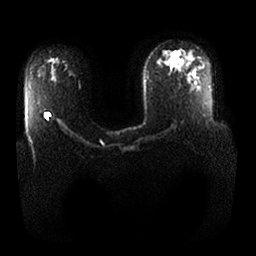
Breast MRI, one axial slice. Slice 13 of 25 in the series (ordered by position). Diffusion-weighted series; image 2 of 4 stored at this slice position (different b-values; order by instance number). 1.5 T. 256 × 256 image matrix, field of view 380 × 380 mm. Female patient.
Structures marked on this image (manually delineated by an expert):
- tumour on diffusion-weighted imaging: bounding box <45,112,51,121> (left, top, right, bottom; pixels)